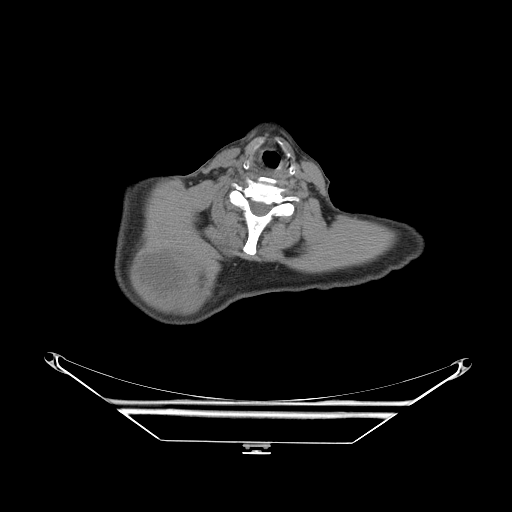
CT of an extremity soft-tissue mass (from a PET/CT study), one axial slice. Position 218 of 267 along the scan axis. Reconstruction kernel STANDARD. 140 kVp. Soft-tissue window (W 400 / L 40 HU). 512 × 512 image matrix. Male patient. Case-level facts recorded for this patient, not image findings: histological type: pleiomorphic spindle cell undifferentiated; grade: high; site of the primary tumour: right parascapusular.
Annotated regions visible in this slice (expert contour drawn on MRI and transferred to this co-registered scan by the dataset authors):
- gross tumour volume including surrounding oedema: box from (x=133, y=247) to (x=218, y=309) px
- gross tumour volume (mass): (x=137, y=254)–(x=191, y=305)